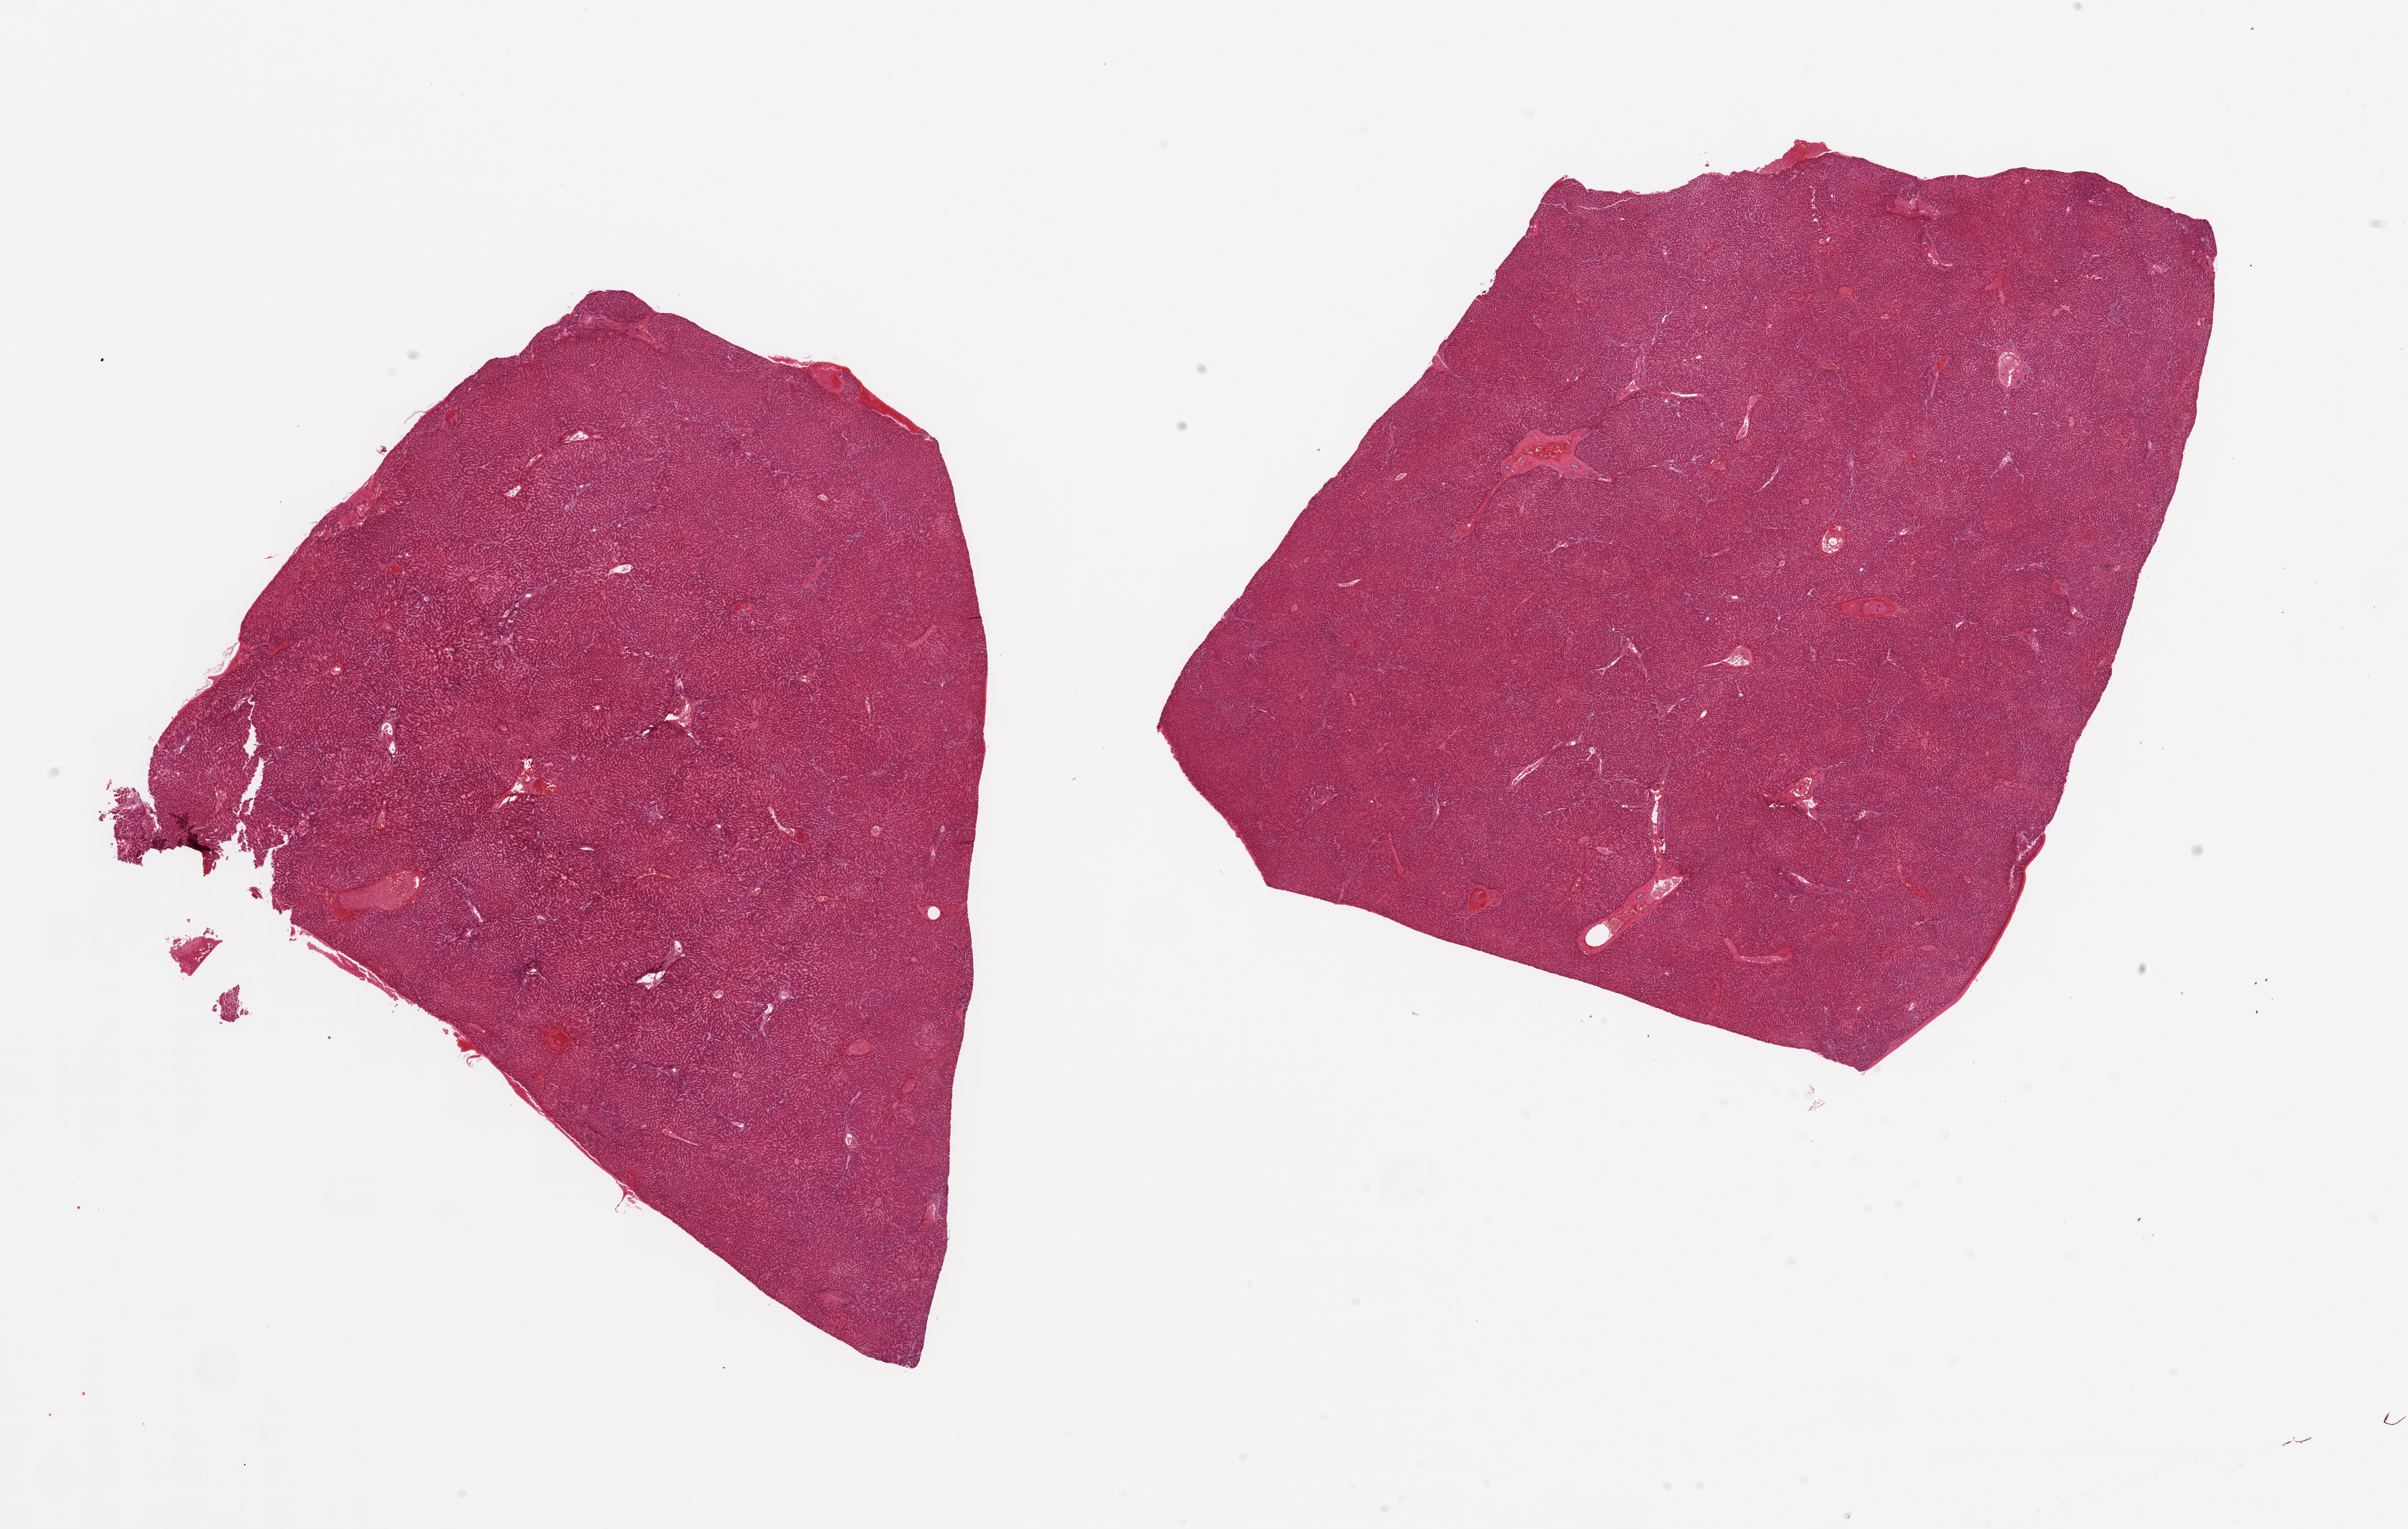
H&E whole-slide image — a low-resolution overview of the entire scanned area, about 26.6 x 16.9 mm, PAXgene-fixed, paraffin-embedded tissue, target tissue: liver, tissue donor sample. Male donor.
• reviewer comment on this tissue sample: 2 pieces, no abnormalities